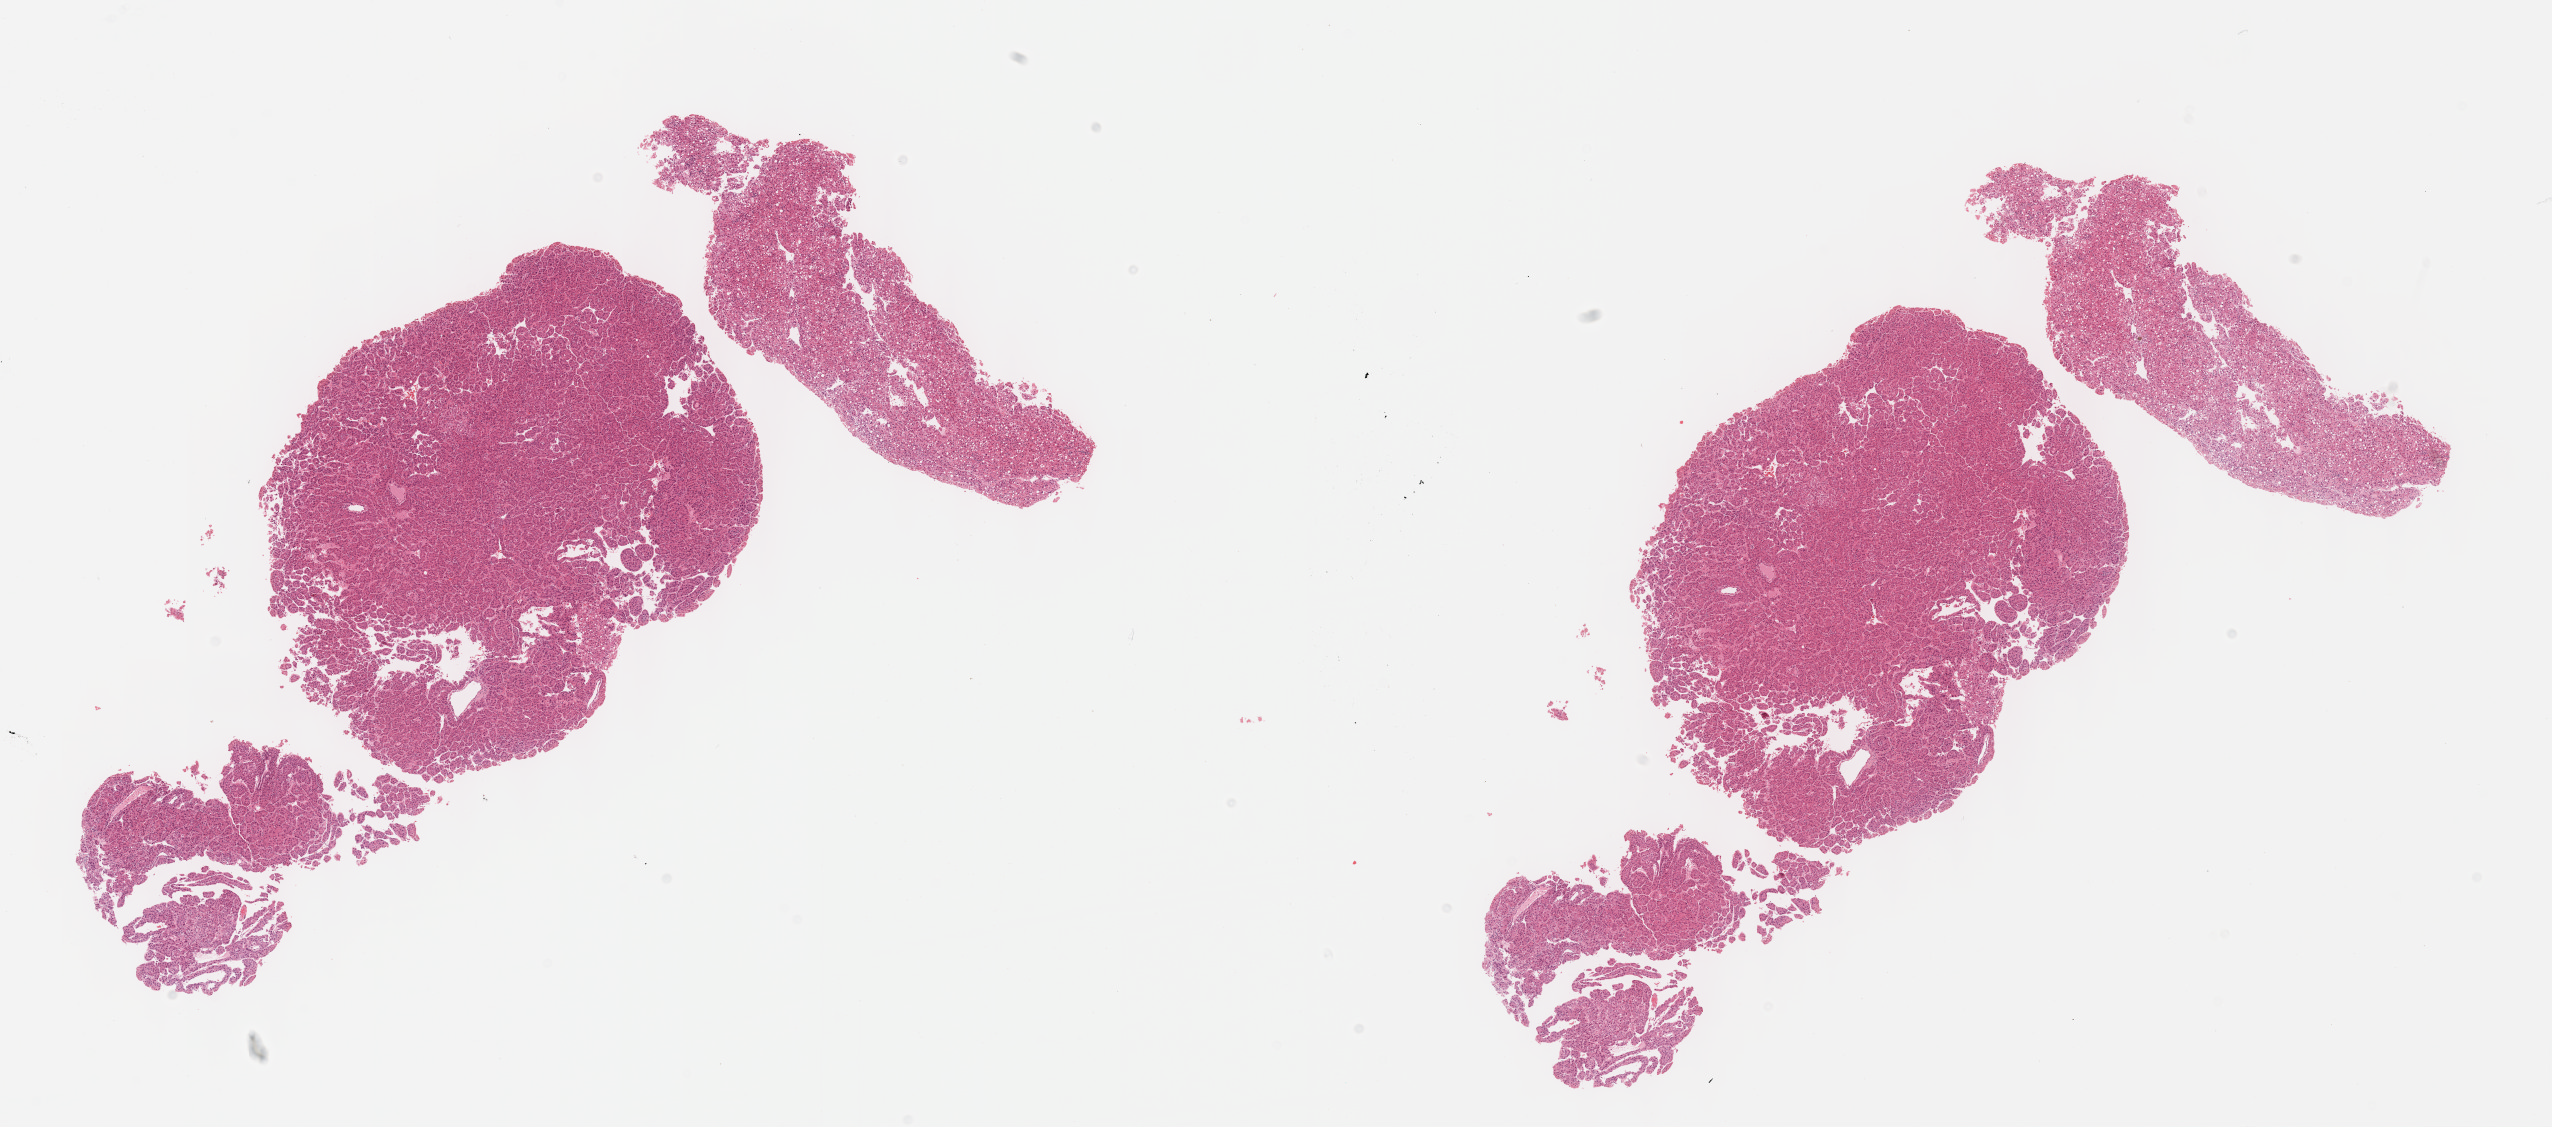
Digitized Hematoxylin and eosin (H&E) stained tissue section (whole slide), low-resolution overview of the scanned area, about 20.6 x 9.1 mm (from a 40x scan); FFPE section; primary tumour sample from the liver. Male patient; age at initial diagnosis 58 years. Histologic grade: G3 (poorly differentiated).
AJCC pathologic stage: I (6th edition). Pathologic diagnosis: Hepatocellular carcinoma, NOS.